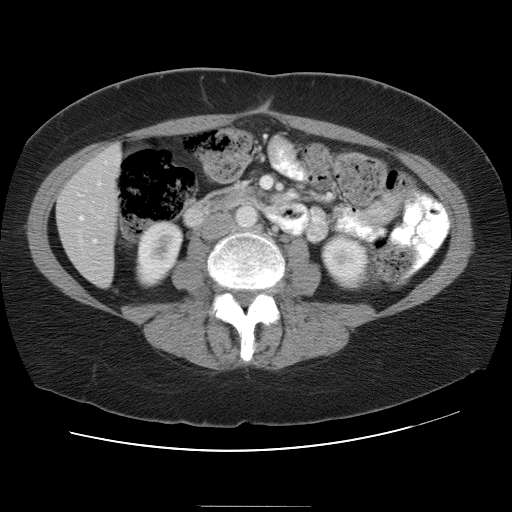
Contrast-enhanced abdominal CT, one axial slice; position 8 of 30 along the scan axis; intravenous contrast given; soft-tissue window (W 400 / L 40 HU); 7.5 mm slice thickness; 512 × 512 image matrix. Female patient, age 52 years. Case-level facts recorded for this patient, not image findings: diagnosis: colorectal cancer liver metastases, imaged before liver resection.
Outlined on this slice (manually delineated by an expert):
- hepatic veins: bounding box (x1, y1, x2, y2) in pixels: (79, 217, 83, 220)
- liver: (58, 146, 122, 286)
- portal vein (with intrahepatic branches): (79, 195, 96, 243)